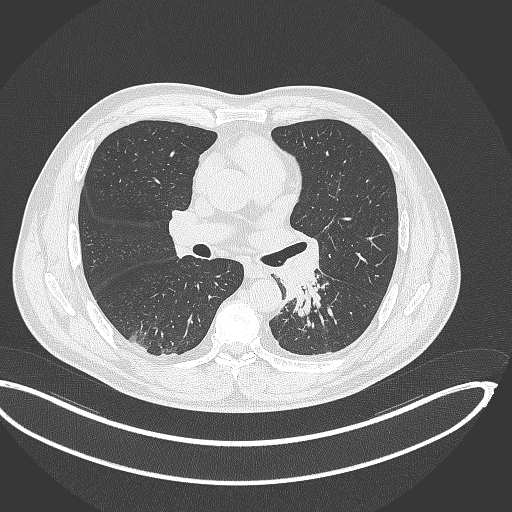
Chest CT, one axial slice. Position 198 of 362 along the scan axis. Reconstruction kernel B70f. 120 kVp. Lung window (W 1500 / L -600 HU). 1 mm slice thickness. 512 × 512 image matrix. Male patient, age 50 years. Case-level facts recorded for this patient, not image findings: clinical TNM (as recorded): T2a N3 M0.
Outlined on this slice (bounding box drawn by a radiologist):
- lung tumour (recorded histology: squamous cell carcinoma): bounding box <276,267,326,318> (left, top, right, bottom; pixels)